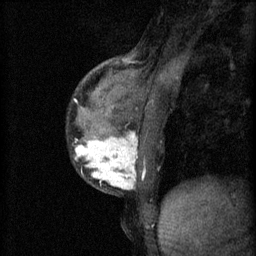
Breast MRI (dynamic contrast-enhanced), one sagittal slice; position 24 of 60 along the scan axis; 3 images stored at this slice position (order not interpretable as contrast timing); 1.5 T; TE 4.2 ms, TR 11 ms; 2 mm slice thickness; 256 × 256 image matrix, field of view 180 × 180 mm. Patient: female, 37 years.
Outlined on this slice (semi-automatic segmentation, software-assisted and operator-edited):
- analysis volume of interest (the breast-tissue region the enhancement analysis was run in; not a lesion): bounding box <68,118,154,193> (left, top, right, bottom; pixels)
- tumour enhancement mask (voxels above the 70 % enhancement threshold inside the analysis volume of interest): <75,132,138,189>